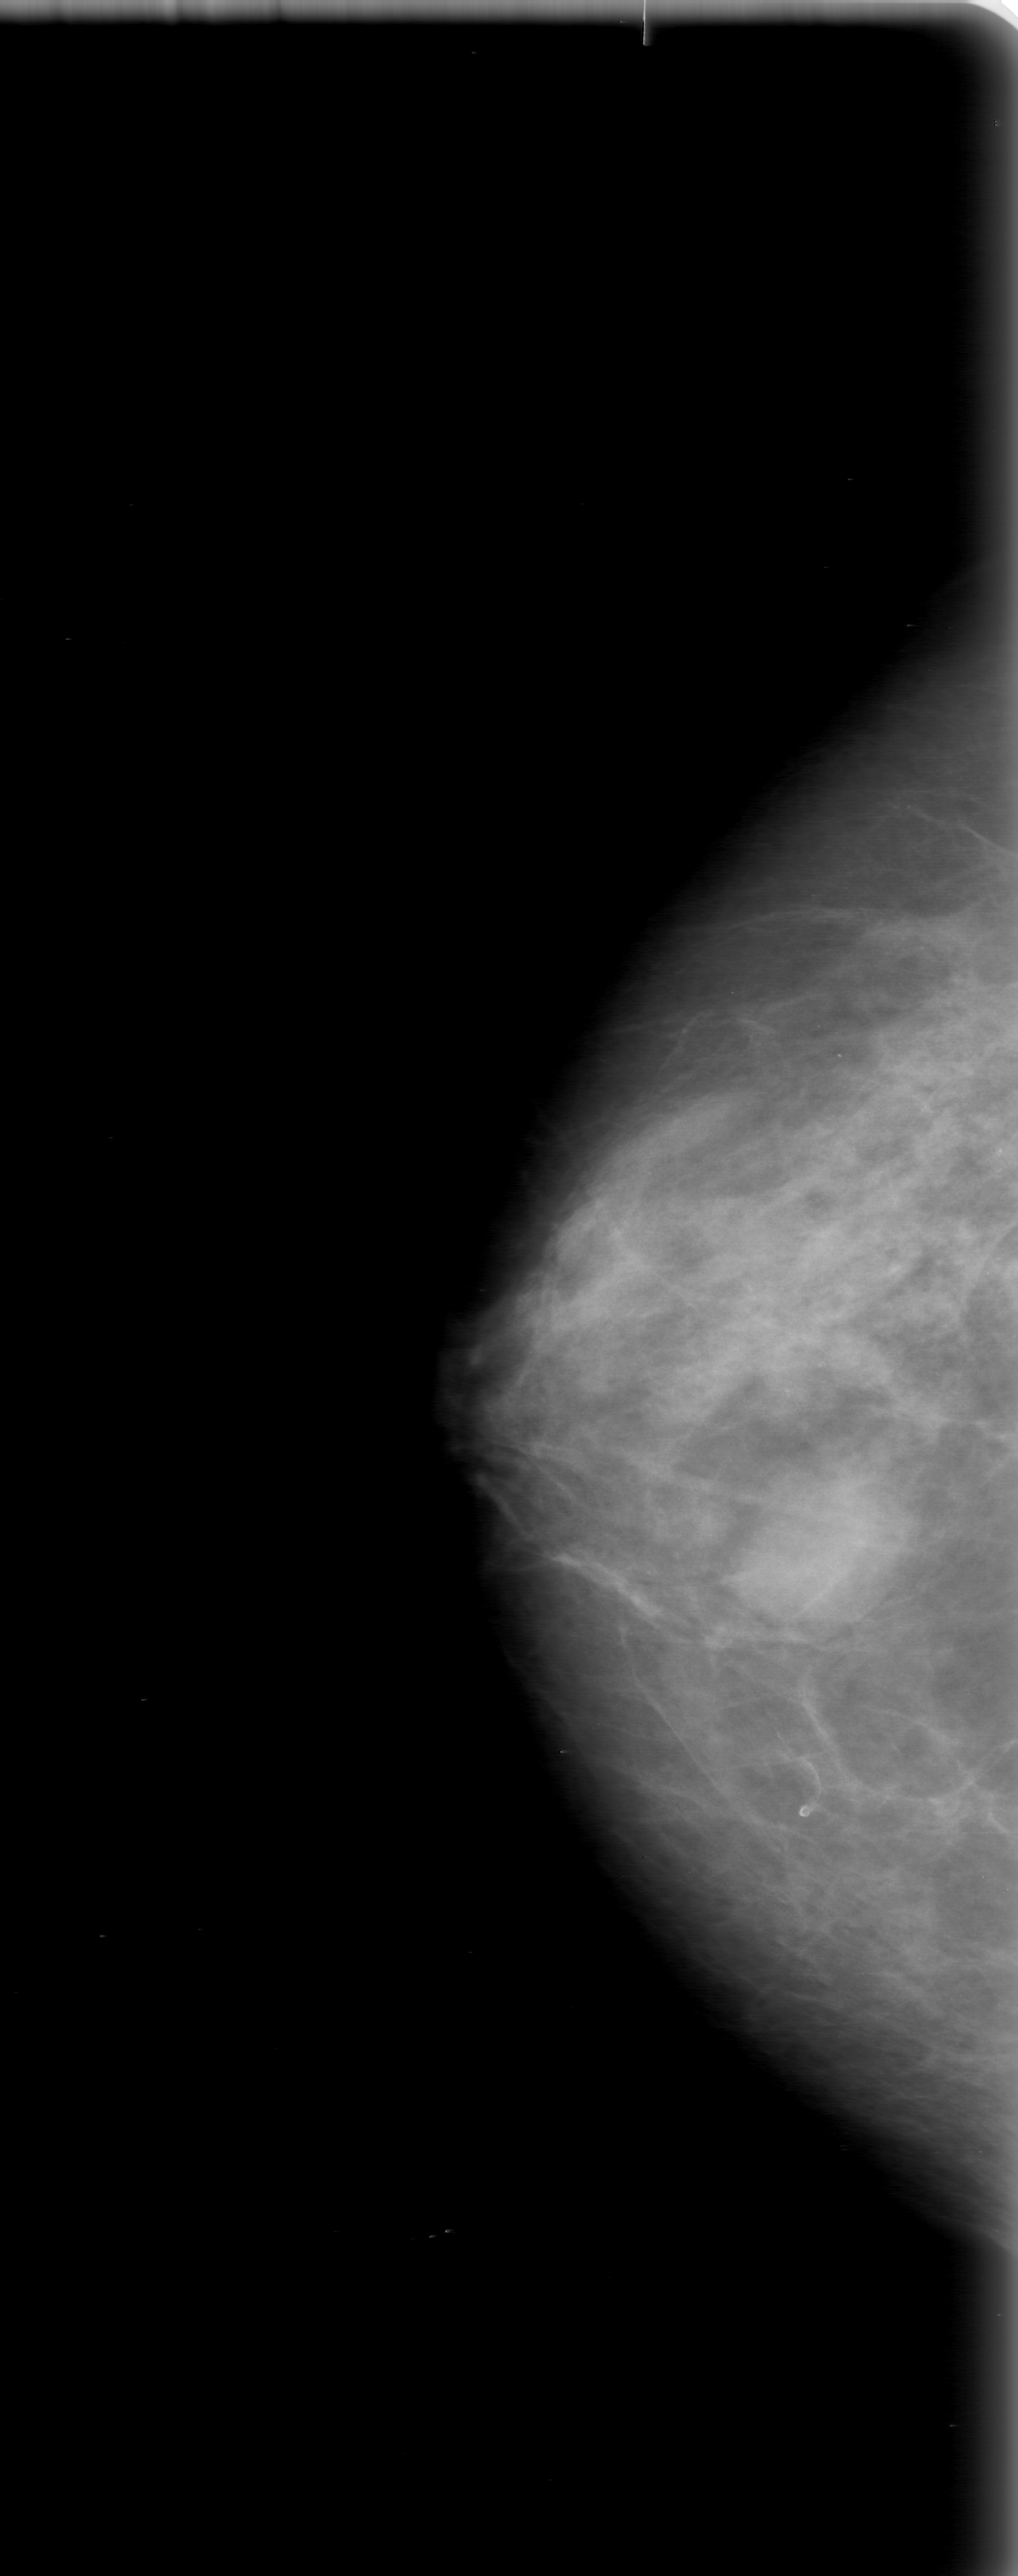
Mammogram (digitized film); right breast; craniocaudal (CC) view; breast composition: heterogeneously dense (BI-RADS density category 3 of 4).
Abnormality record for this image: mass, shape oval, margins obscured; BI-RADS assessment category 0 (incomplete: needs additional imaging); subtlety rating 5 on a 1 (subtle) to 5 (obvious) scale; pathology (as recorded): benign.